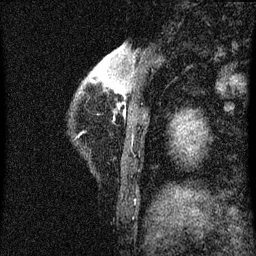
Breast MRI (dynamic contrast-enhanced), one sagittal slice; position 10 of 60 along the scan axis; dynamic contrast-enhanced series, image 2 of 3 at this slice position (ordered by acquisition); 1.5 T; TE 4.2 ms, TR 8 ms; 2 mm slice thickness; 256 × 256 image matrix, field of view 180 × 180 mm. Patient: female, 38 years.
Outlined on this slice (semi-automatically segmented with operator editing):
- analysis volume of interest (the breast-tissue region the enhancement analysis was run in; not a lesion): bounding box <78,46,136,125> (left, top, right, bottom; pixels)
- tumour enhancement mask (voxels above the 70 % enhancement threshold inside the analysis volume of interest): <115,88,124,93>